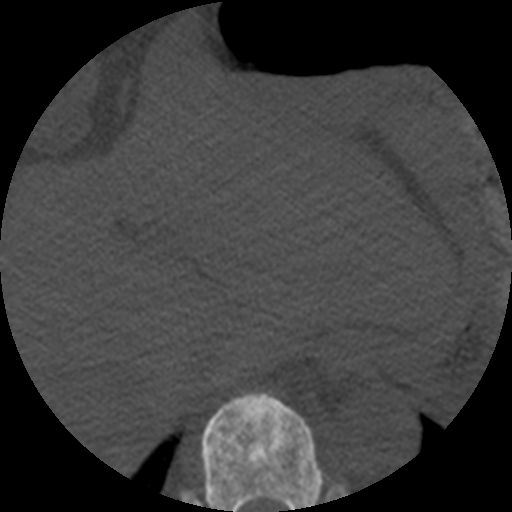
CT including the spine, one axial slice; slice 269 of 508 in the series (ordered by position); bone window (W 1800 / L 400 HU); 1.25 mm slice thickness; 512 × 512 image matrix. Patient age 57 years. From the clinical record (not read from this slice): primary cancer: prostate.
Structures marked on this image (semi-automatic segmentation, software-assisted and operator-edited):
- T10 vertebra: bounding box <201,392,322,512> (left, top, right, bottom; pixels)